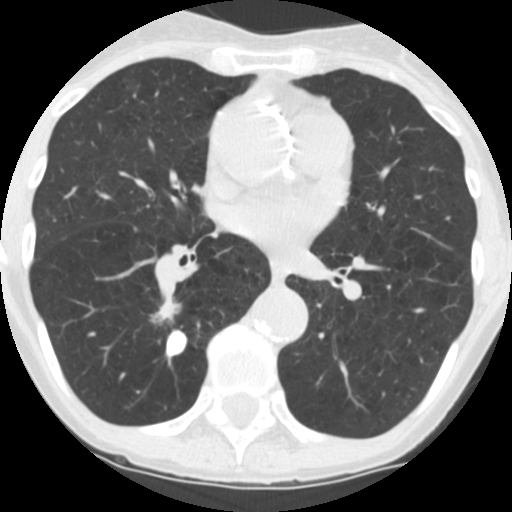
Low-dose screening chest CT, one axial slice. Position 60 of 124 along the scan axis. 120 kVp. Lung window (W 1500 / L -600 HU). 2.5 mm slice thickness. 512 × 512 image matrix, field of view 260 × 260 mm.
Structures marked on this image (outlined manually by an expert reader):
- lesion 1 (tumor, lower lobe of right lung): box from (x=157, y=301) to (x=178, y=320) px